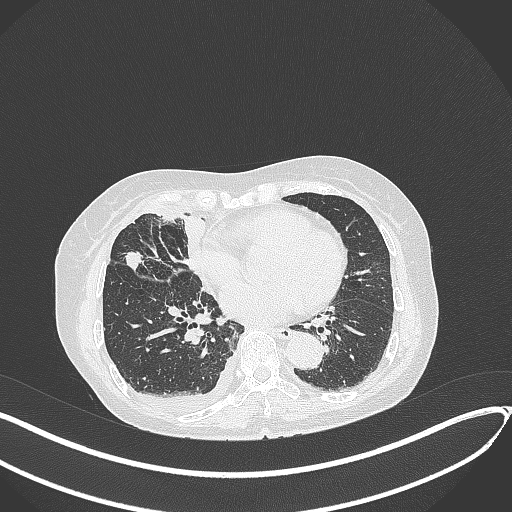
Chest CT, one axial slice; slice 161 of 418 in the series (ordered by position); reconstruction kernel B70f; 120 kVp; lung window (W 1500 / L -600 HU); 512 × 512 image matrix, field of view 400 × 400 mm. Female patient, age 75 years. From the clinical record (not read from this slice): clinical TNM (as recorded): T2a N3 M0.
Annotated regions visible in this slice (bounding box drawn by a radiologist):
- lung tumour (recorded histology: adenocarcinoma): bounding box [x1, y1, x2, y2] px = [122, 247, 144, 279]